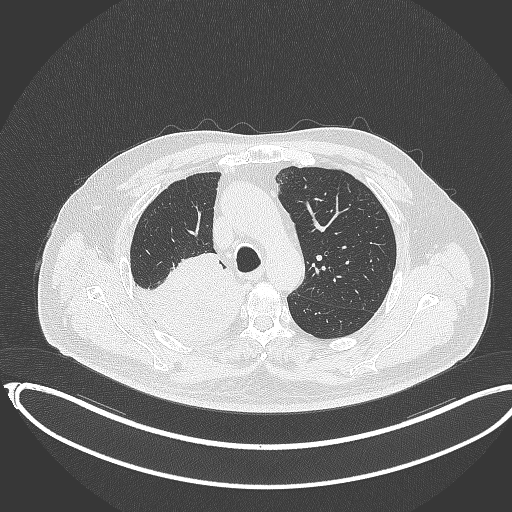
Chest CT, one axial slice; slice 261 of 403 in the series (ordered by position); reconstruction kernel B70f; 120 kVp; lung window (W 1500 / L -600 HU); 1 mm slice thickness; 512 × 512 image matrix, field of view 436 × 436 mm. Patient: male, 68 years. Case-level facts recorded for this patient, not image findings: clinical TNM (as recorded): T2a N0 M0.
Structures marked on this image (bounding box drawn by a radiologist):
- lung tumour (recorded histology: adenocarcinoma): box from (x=134, y=255) to (x=250, y=342) px